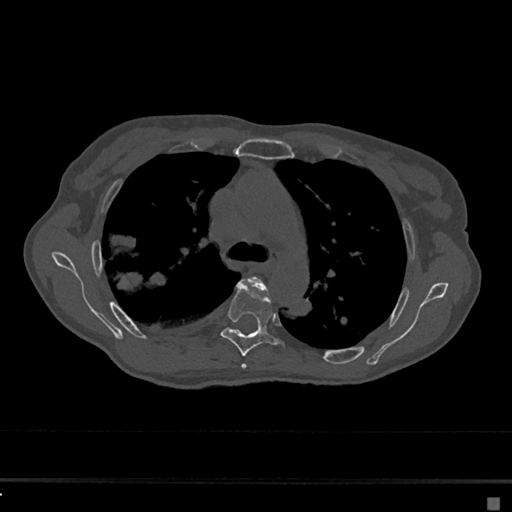
CT including the spine, one axial slice; position 464 of 797 along the scan axis; reconstruction kernel Br40s/3; 120 kVp; bone window (W 1800 / L 400 HU); 512 × 512 image matrix, field of view 360 × 360 mm. Patient: female, 68 years. From the clinical record (not read from this slice): primary cancer: renal.
Annotated regions visible in this slice (semi-automatically segmented with operator editing):
- T4 vertebra: bounding box (x1, y1, x2, y2) in pixels: (241, 276, 270, 370)
- T5 vertebra: (220, 283, 283, 356)